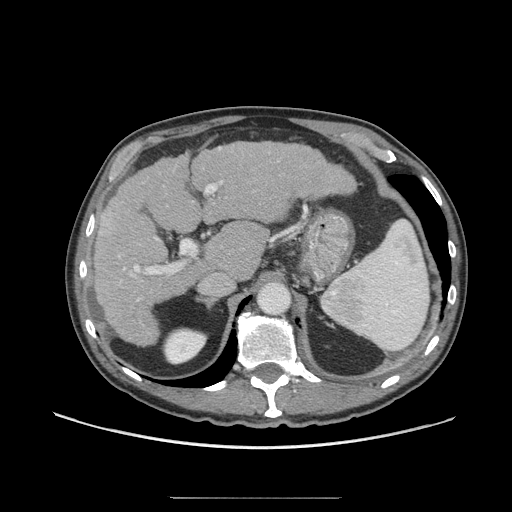
Contrast-enhanced abdominal CT (liver protocol), one axial slice. Slice 43 of 71 in the series (ordered by position). Reconstruction kernel STANDARD. Soft-tissue window (W 400 / L 40 HU). 512 × 512 image matrix. Case-level facts recorded for this patient, not image findings: diagnosis: hepatocellular carcinoma (patient treated with transarterial chemoembolisation; whether this scan precedes or follows treatment is not stated here); TNM stage (as recorded): Stage-I; Child-Pugh class: A; tumour differentiation: well differentiated; tumour nodularity: uninodular.
Structures marked on this image (semi-automatic segmentation, software-assisted and operator-edited):
- liver parenchyma outside the tumour (the mass and vessels are separate outlines, so this box may not span the whole liver): bounding box [x1, y1, x2, y2] px = [92, 142, 354, 345]
- mass: [101, 215, 116, 235]
- liver vessels: [123, 148, 223, 301]